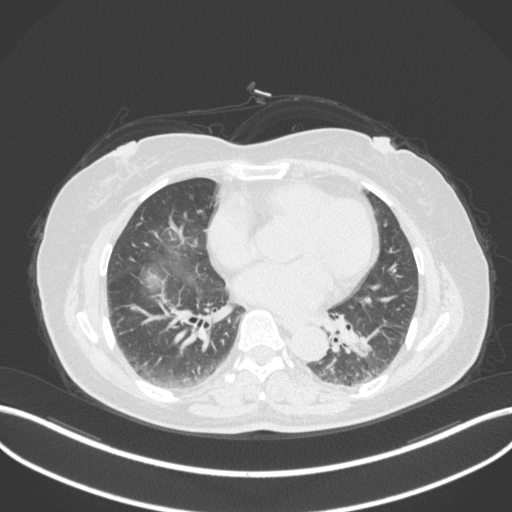
Chest CT, one axial slice. Slice 162 of 307 in the series (ordered by position). Reconstruction kernel B31f. Lung window (W 1500 / L -600 HU). 1 mm slice thickness. 512 × 512 image matrix, field of view 400 × 400 mm. Patient: female, 59 years. Case-level facts recorded for this patient, not image findings: clinical TNM (as recorded): T2a N0 M0.
Annotated regions visible in this slice (bounding box drawn by a radiologist):
- lung tumour (recorded histology: adenocarcinoma): bounding box <346,323,385,360> (left, top, right, bottom; pixels)